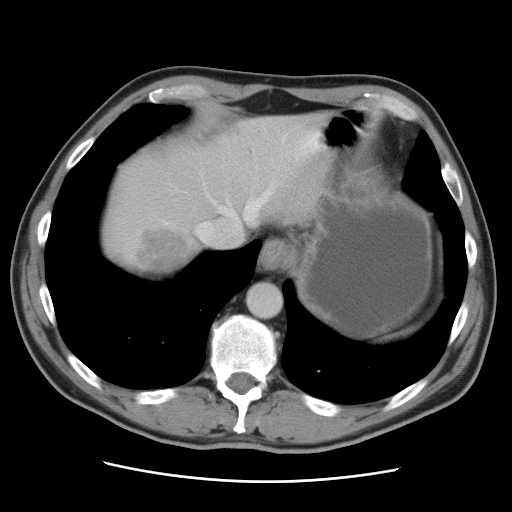
Contrast-enhanced abdominal CT, one axial slice. Position 78 of 89 along the scan axis. 120 kVp. Intravenous contrast given. Soft-tissue window (W 400 / L 40 HU). 5 mm slice thickness. 512 × 512 image matrix, field of view 366 × 366 mm. Male patient, age 59 years. From the clinical record (not read from this slice): diagnosis: colorectal cancer liver metastases, imaged before liver resection; multiple liver metastases: yes; largest metastasis: 0.6 cm; chemotherapy before resection: no.
Structures marked on this image (outlined manually by an expert reader):
- hepatic veins: bounding box [x1, y1, x2, y2] px = [196, 134, 288, 243]
- liver: [100, 112, 333, 280]
- planned liver remnant (the part of the liver to remain after resection): [137, 112, 333, 229]
- liver metastasis: [134, 233, 202, 274]